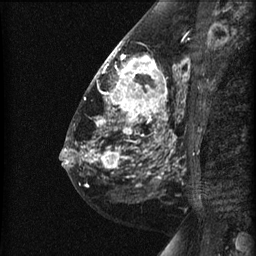
Breast MRI (dynamic contrast-enhanced), one sagittal slice; position 26 of 60 along the scan axis; dynamic contrast-enhanced series, image 2 of 3 at this slice position (ordered by acquisition); 1.5 T; TE 4.2 ms, TR 22.7 ms; 256 × 256 image matrix. Female patient, age 48 years. Case-level facts recorded for this patient, not image findings: setting: breast cancer imaged before/during neoadjuvant chemotherapy; receptor status: triple-negative.
Structures marked on this image (semi-automatically segmented with operator editing):
- analysis volume of interest (the breast-tissue region the enhancement analysis was run in; not a lesion): bounding box <89,27,191,180> (left, top, right, bottom; pixels)
- tumour enhancement mask (voxels above the 90 % enhancement threshold inside the analysis volume of interest): <94,48,180,168>